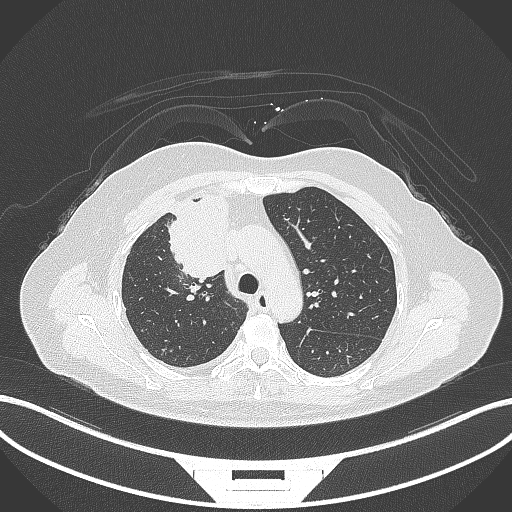
Chest CT, one axial slice. Position 209 of 305 along the scan axis. Reconstruction kernel B70f. Lung window (W 1500 / L -600 HU). 1 mm slice thickness. 512 × 512 image matrix. Patient: female, 52 years. From the clinical record (not read from this slice): clinical TNM (as recorded): T3 N1 M1.
Structures marked on this image (rectangle marked by the reading radiologist):
- lung tumour (recorded histology: adenocarcinoma): box from (x=164, y=196) to (x=235, y=284) px